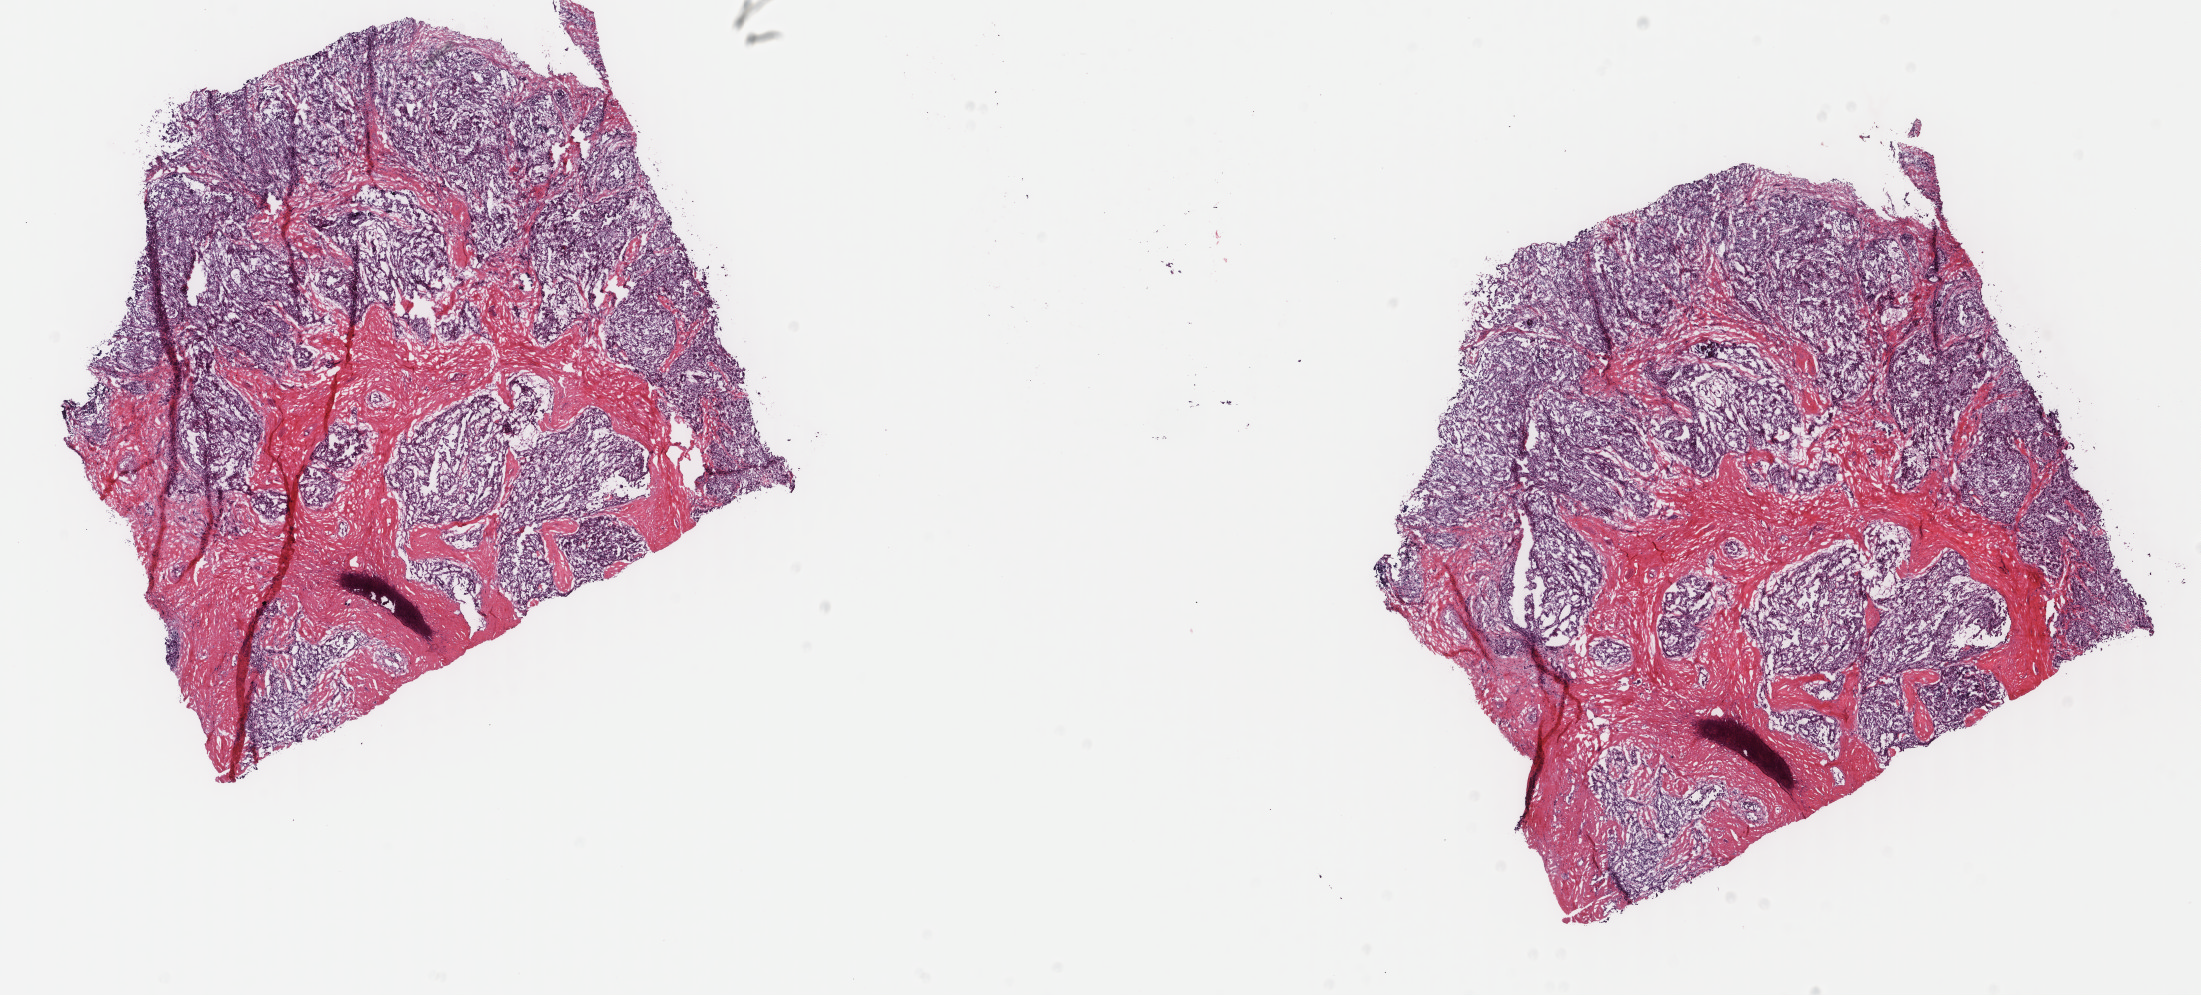
Whole-slide histology image, H&E, low-resolution overview of the scanned area, about 17.5 x 7.9 mm, frozen section, primary tumour sample from the thyroid. Patient: female, age at initial diagnosis 46 years. Pathologist review of this section (percent, as recorded): tumour cells 100%, tumour nuclei 80%, normal cells 0%, stromal cells 0%, necrosis 0%. Inflammatory infiltration, as recorded: lymphocyte infiltration 0%, monocyte infiltration 0%, neutrophil infiltration 0%.
- AJCC pathologic stage: III (7th edition)
- lymph nodes positive (case pathology): 1 of 16 examined
- diagnosis: Papillary adenocarcinoma, NOS (thyroid gland)